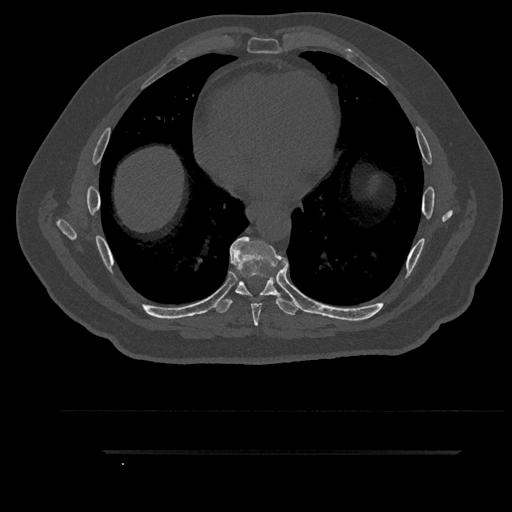
CT including the spine, one axial slice. Slice 501 of 797 in the series (ordered by position). Bone window (W 1800 / L 400 HU). 0.5 mm slice thickness. 512 × 512 image matrix, field of view 432 × 432 mm. Male patient, age 63 years. From the clinical record (not read from this slice): primary cancer: renal; vertebrae with lytic lesions (as recorded): T8.
Structures marked on this image (semi-automatic segmentation, software-assisted and operator-edited):
- T6 vertebra: bounding box (x1, y1, x2, y2) in pixels: (251, 292, 262, 296)
- T7 vertebra: (230, 236, 288, 326)
- T8 vertebra: (214, 248, 300, 315)